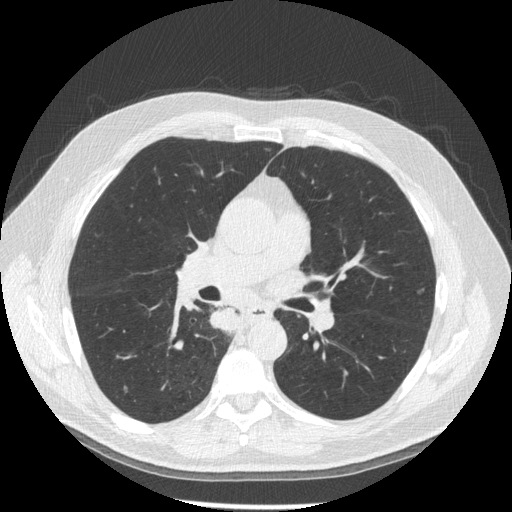
Chest CT (low-dose screening protocol), one axial image. Third annual screen. Lung window (W 1500 / L -600 HU). 1.25 mm slice thickness. Standard (soft-tissue) reconstruction kernel (STANDARD). Slice 79 of 181 in the series. Male participant, aged 61 years at enrolment. Former smoker at enrolment.
Expert-annotated lung lesion, bounding box [x1, y1, x2, y2] px = [207, 298, 256, 345]. Screening reader's record for this exam: no non-calcified nodule ≥4 mm recorded. Participant outcome: lung cancer diagnosed 10 days after this screen — squamous cell carcinoma, keratinizing, NOS, right lower lobe, stage IIIB (AJCC 6th edition), 40 mm at pathology.